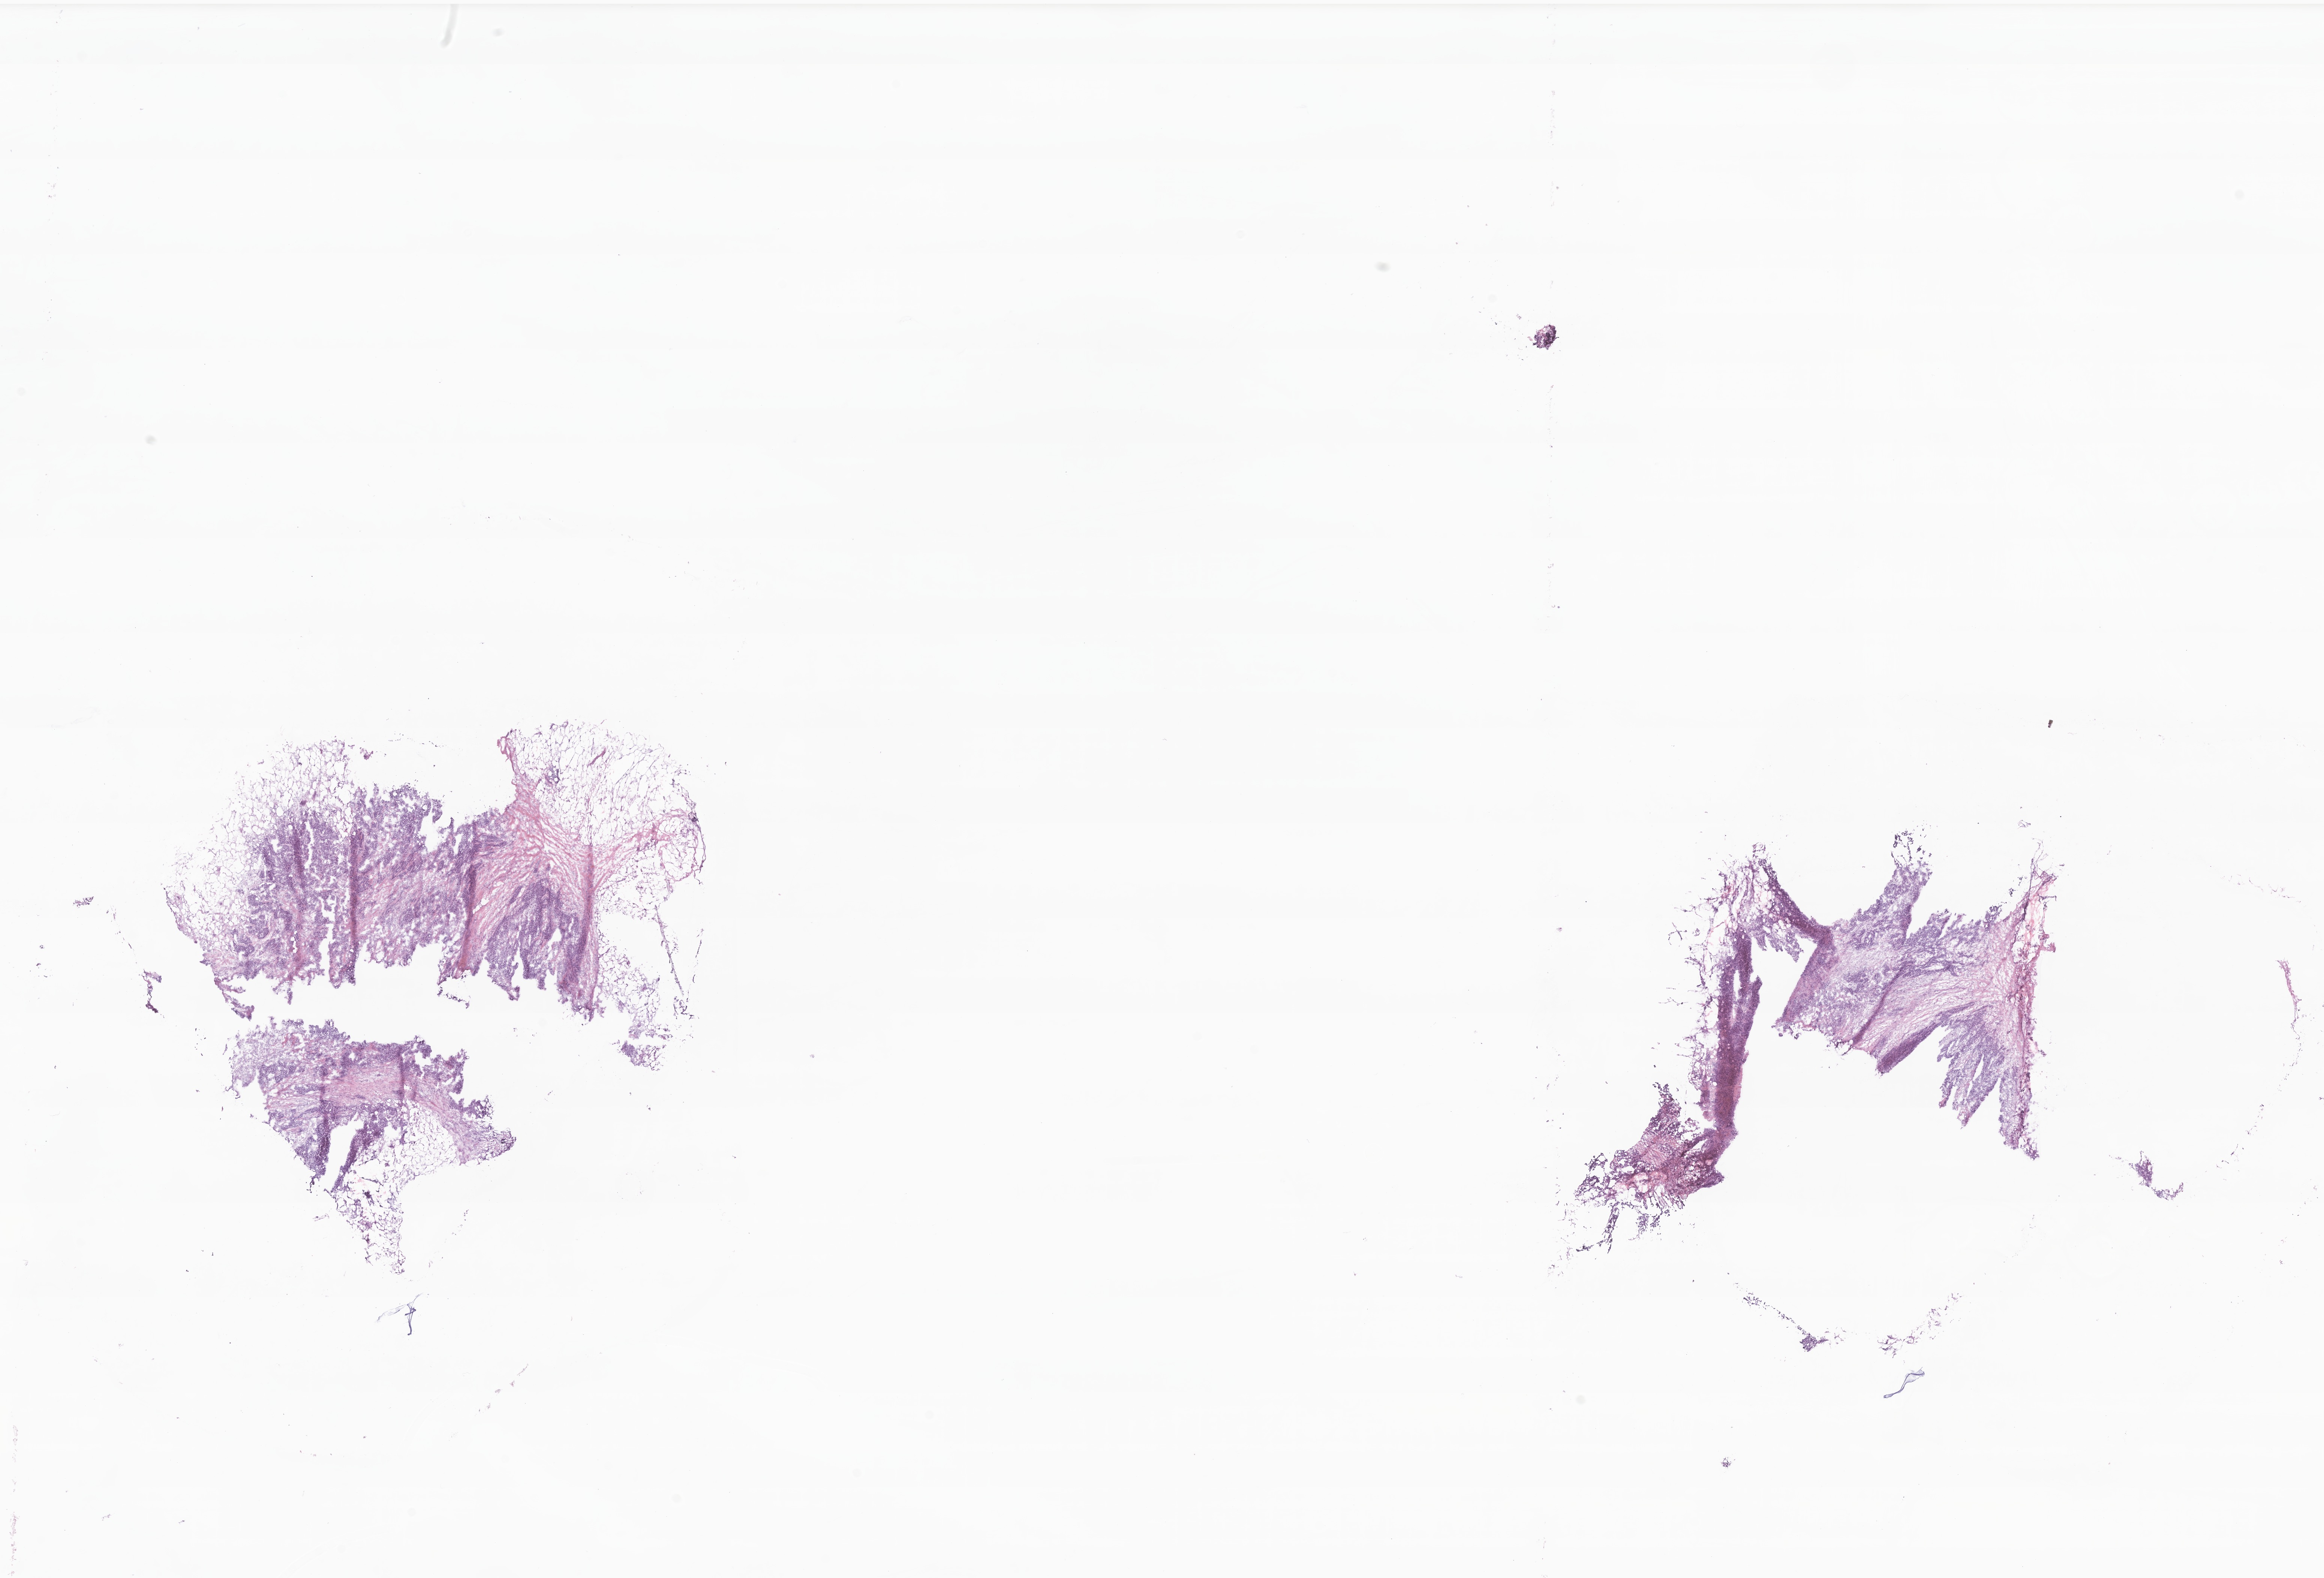
Hematoxylin and eosin (H&E) whole-slide image, low-resolution overview of the scanned area, about 26.2 x 17.8 mm; cryosection; specimen: primary tumor; anatomic site: breast (right). Female, age 77 years at initial diagnosis. Pathologist review of this section (percent, as recorded): tumor cells 35%, tumor nuclei 82%, stromal cells 64%, necrosis 1%, normal cells 0%. Infiltration values recorded for this section: lymphocyte infiltration 12%, monocyte infiltration 2%, neutrophil infiltration 0%.
- histologic diagnosis: Infiltrating duct carcinoma, NOS
- section: bottom of the tissue portion